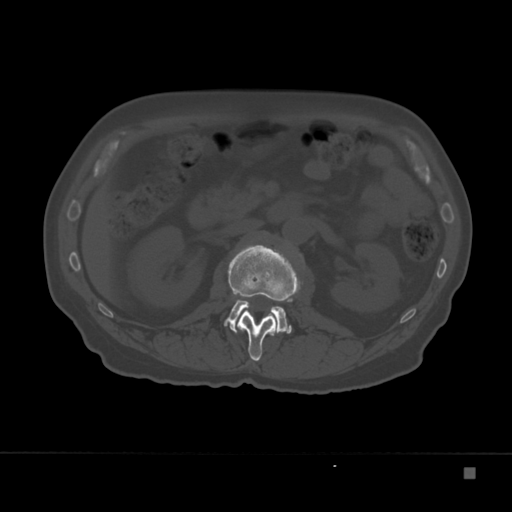
CT including the spine, one axial slice; position 102 of 332 along the scan axis; reconstruction kernel Br40s; bone window (W 1800 / L 400 HU); 1.5 mm slice thickness; 512 × 512 image matrix, field of view 389 × 389 mm. Male patient, age 72 years. Case-level facts recorded for this patient, not image findings: primary cancer: skeletal.
Outlined on this slice (semi-automatic segmentation, software-assisted and operator-edited):
- L1 vertebra: box from (x=228, y=244) to (x=301, y=361) px
- L2 vertebra: (x=224, y=300)–(x=292, y=333)